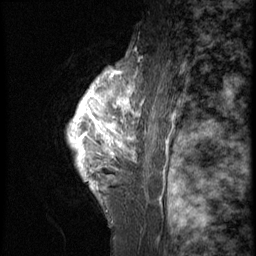
Breast MRI (dynamic contrast-enhanced), one sagittal slice; position 45 of 58 along the scan axis; 3 images stored at this slice position (order not interpretable as contrast timing); 1.5 T; TE 4.2 ms, TR 9 ms; 256 × 256 image matrix. Patient: female, 50 years. Case-level facts recorded for this patient, not image findings: setting: breast cancer imaged before/during neoadjuvant chemotherapy; receptor status: triple-negative.
Annotated regions visible in this slice (semi-automatically segmented with operator editing):
- analysis volume of interest (the breast-tissue region the enhancement analysis was run in; not a lesion): bounding box (x1, y1, x2, y2) in pixels: (67, 52, 128, 214)
- tumour enhancement mask (voxels above the 140 % enhancement threshold inside the analysis volume of interest): (68, 65, 128, 178)